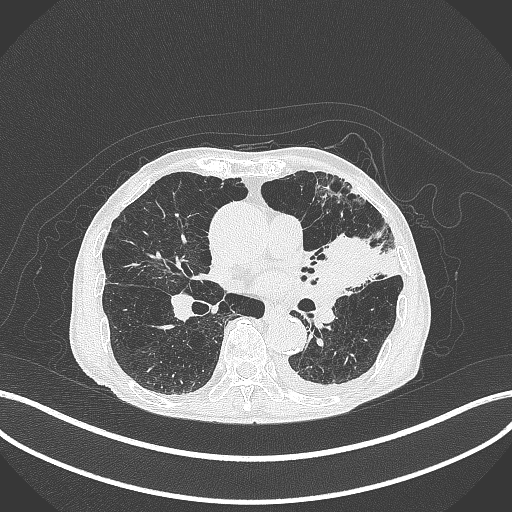
Chest CT, one axial slice; position 194 of 385 along the scan axis; reconstruction kernel B70f; 120 kVp; lung window (W 1500 / L -600 HU); 512 × 512 image matrix. Male patient, age 90 years or older. From the clinical record (not read from this slice): clinical TNM (as recorded): T2b N1 M0.
Outlined on this slice (bounding box drawn by a radiologist):
- lung tumour (recorded histology: squamous cell carcinoma): bounding box <319,228,380,289> (left, top, right, bottom; pixels)